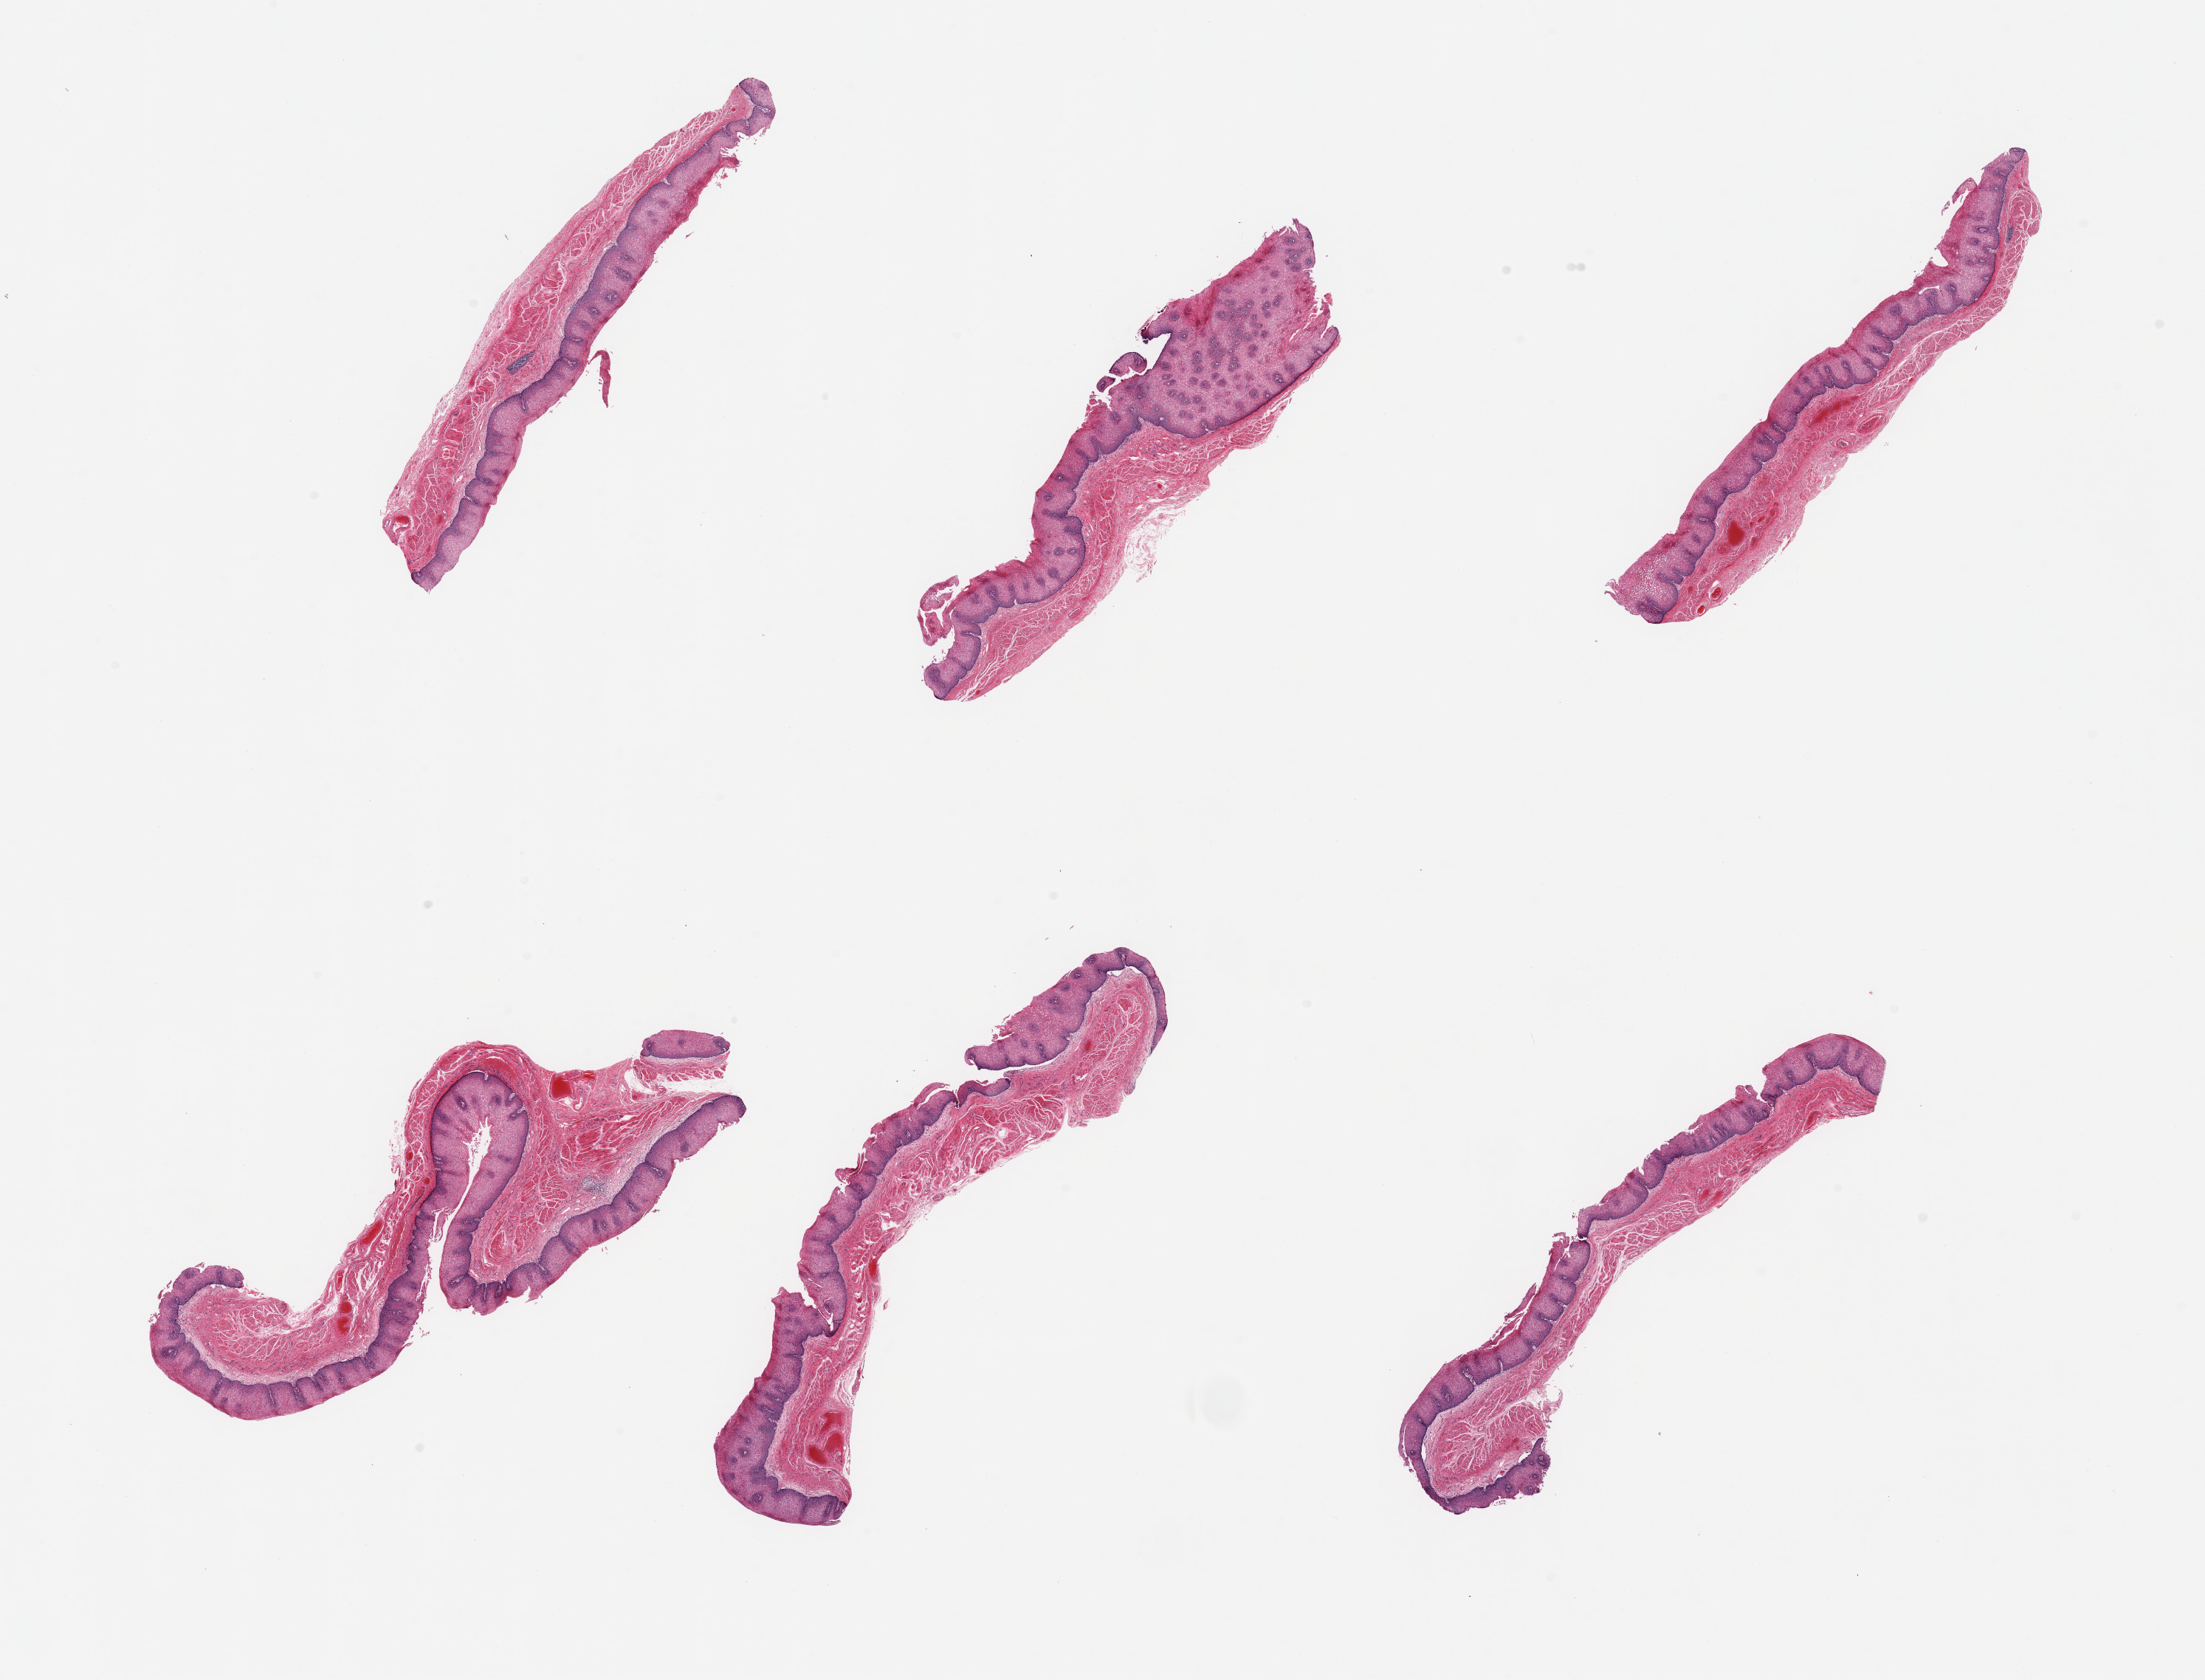
Digitized haematoxylin and eosin-stained section, low-resolution overview of the scanned area, about 23.6 x 18.0 mm; PAXgene-fixed paraffin-embedded (PFPE) section; target tissue: esophageal mucous membrane; donor tissue sample. Donor sex: male.
• pathologist's review note for this sample: 6 pieces squamous mucosa up to ~0.5mm, ~40-50% thickness